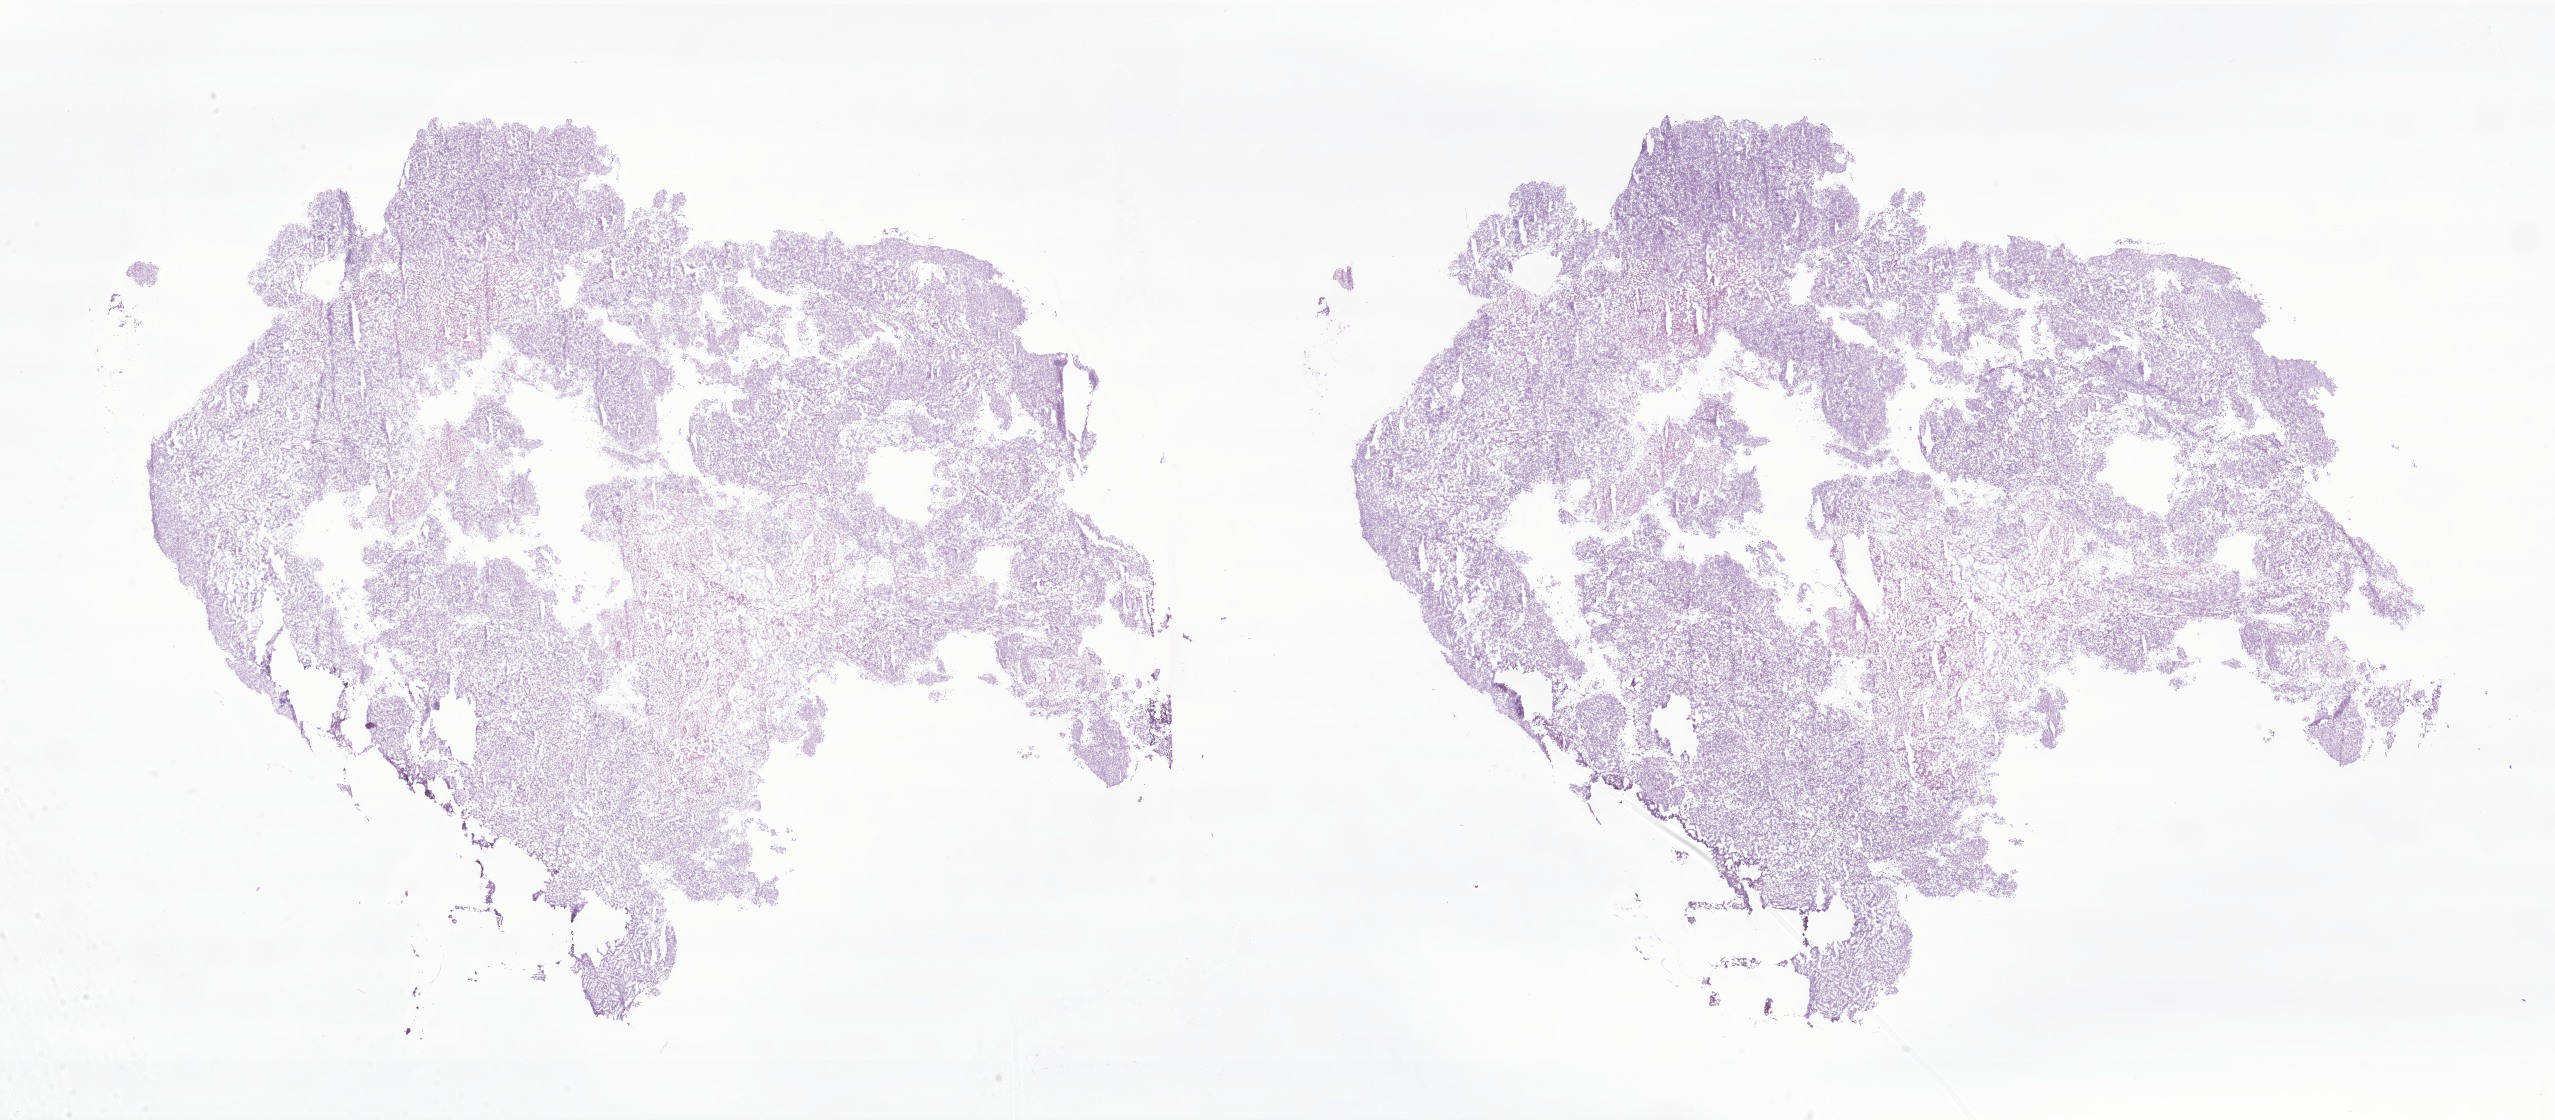
Haematoxylin and eosin whole-slide image of tumor tissue from the spinal cord, a low-resolution overview of the entire scanned area, about 43.1 x 18.9 mm. Frozen section. Patient: female, age 97 months (8 years 1 month).
Recorded diagnosis: Atypical teratoid/rhabdoid tumor.